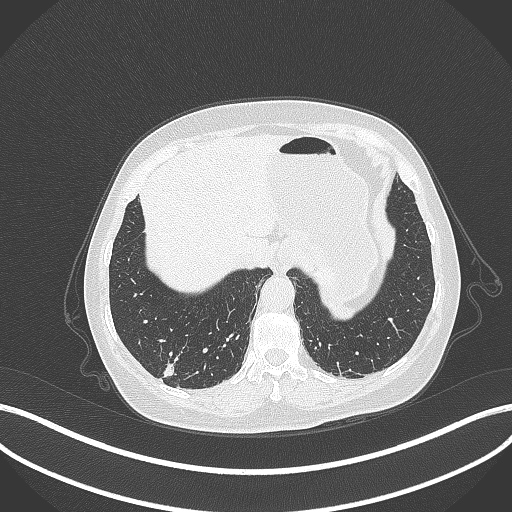
Chest CT, one axial slice; position 46 of 333 along the scan axis; reconstruction kernel B70f; 120 kVp; lung window (W 1500 / L -600 HU); 1 mm slice thickness; 512 × 512 image matrix, field of view 400 × 400 mm. Female patient, age 69 years. From the clinical record (not read from this slice): clinical TNM (as recorded): T1b N0 M0.
Structures marked on this image (rectangle marked by the reading radiologist):
- lung tumour (recorded histology: adenocarcinoma): bounding box <162,357,174,380> (left, top, right, bottom; pixels)